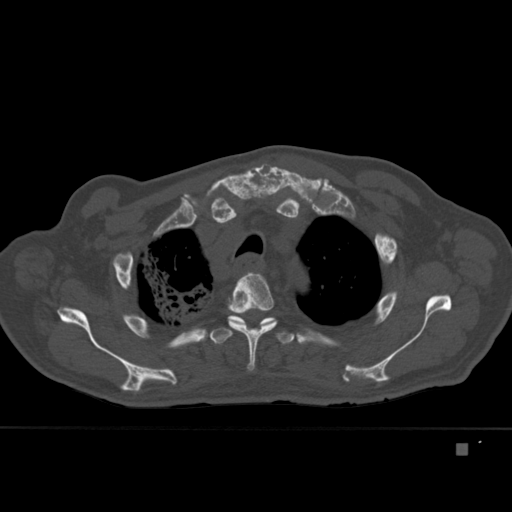
CT including the spine, one axial slice. Slice 331 of 451 in the series (ordered by position). Bone window (W 1800 / L 400 HU). 512 × 512 image matrix, field of view 378 × 378 mm. Male patient, age 75 years. Case-level facts recorded for this patient, not image findings: primary cancer: prostate.
Structures marked on this image (semi-automatic segmentation, software-assisted and operator-edited):
- T3 vertebra: box from (x=228, y=272) to (x=277, y=371) px
- T4 vertebra: (x=210, y=315)–(x=295, y=344)